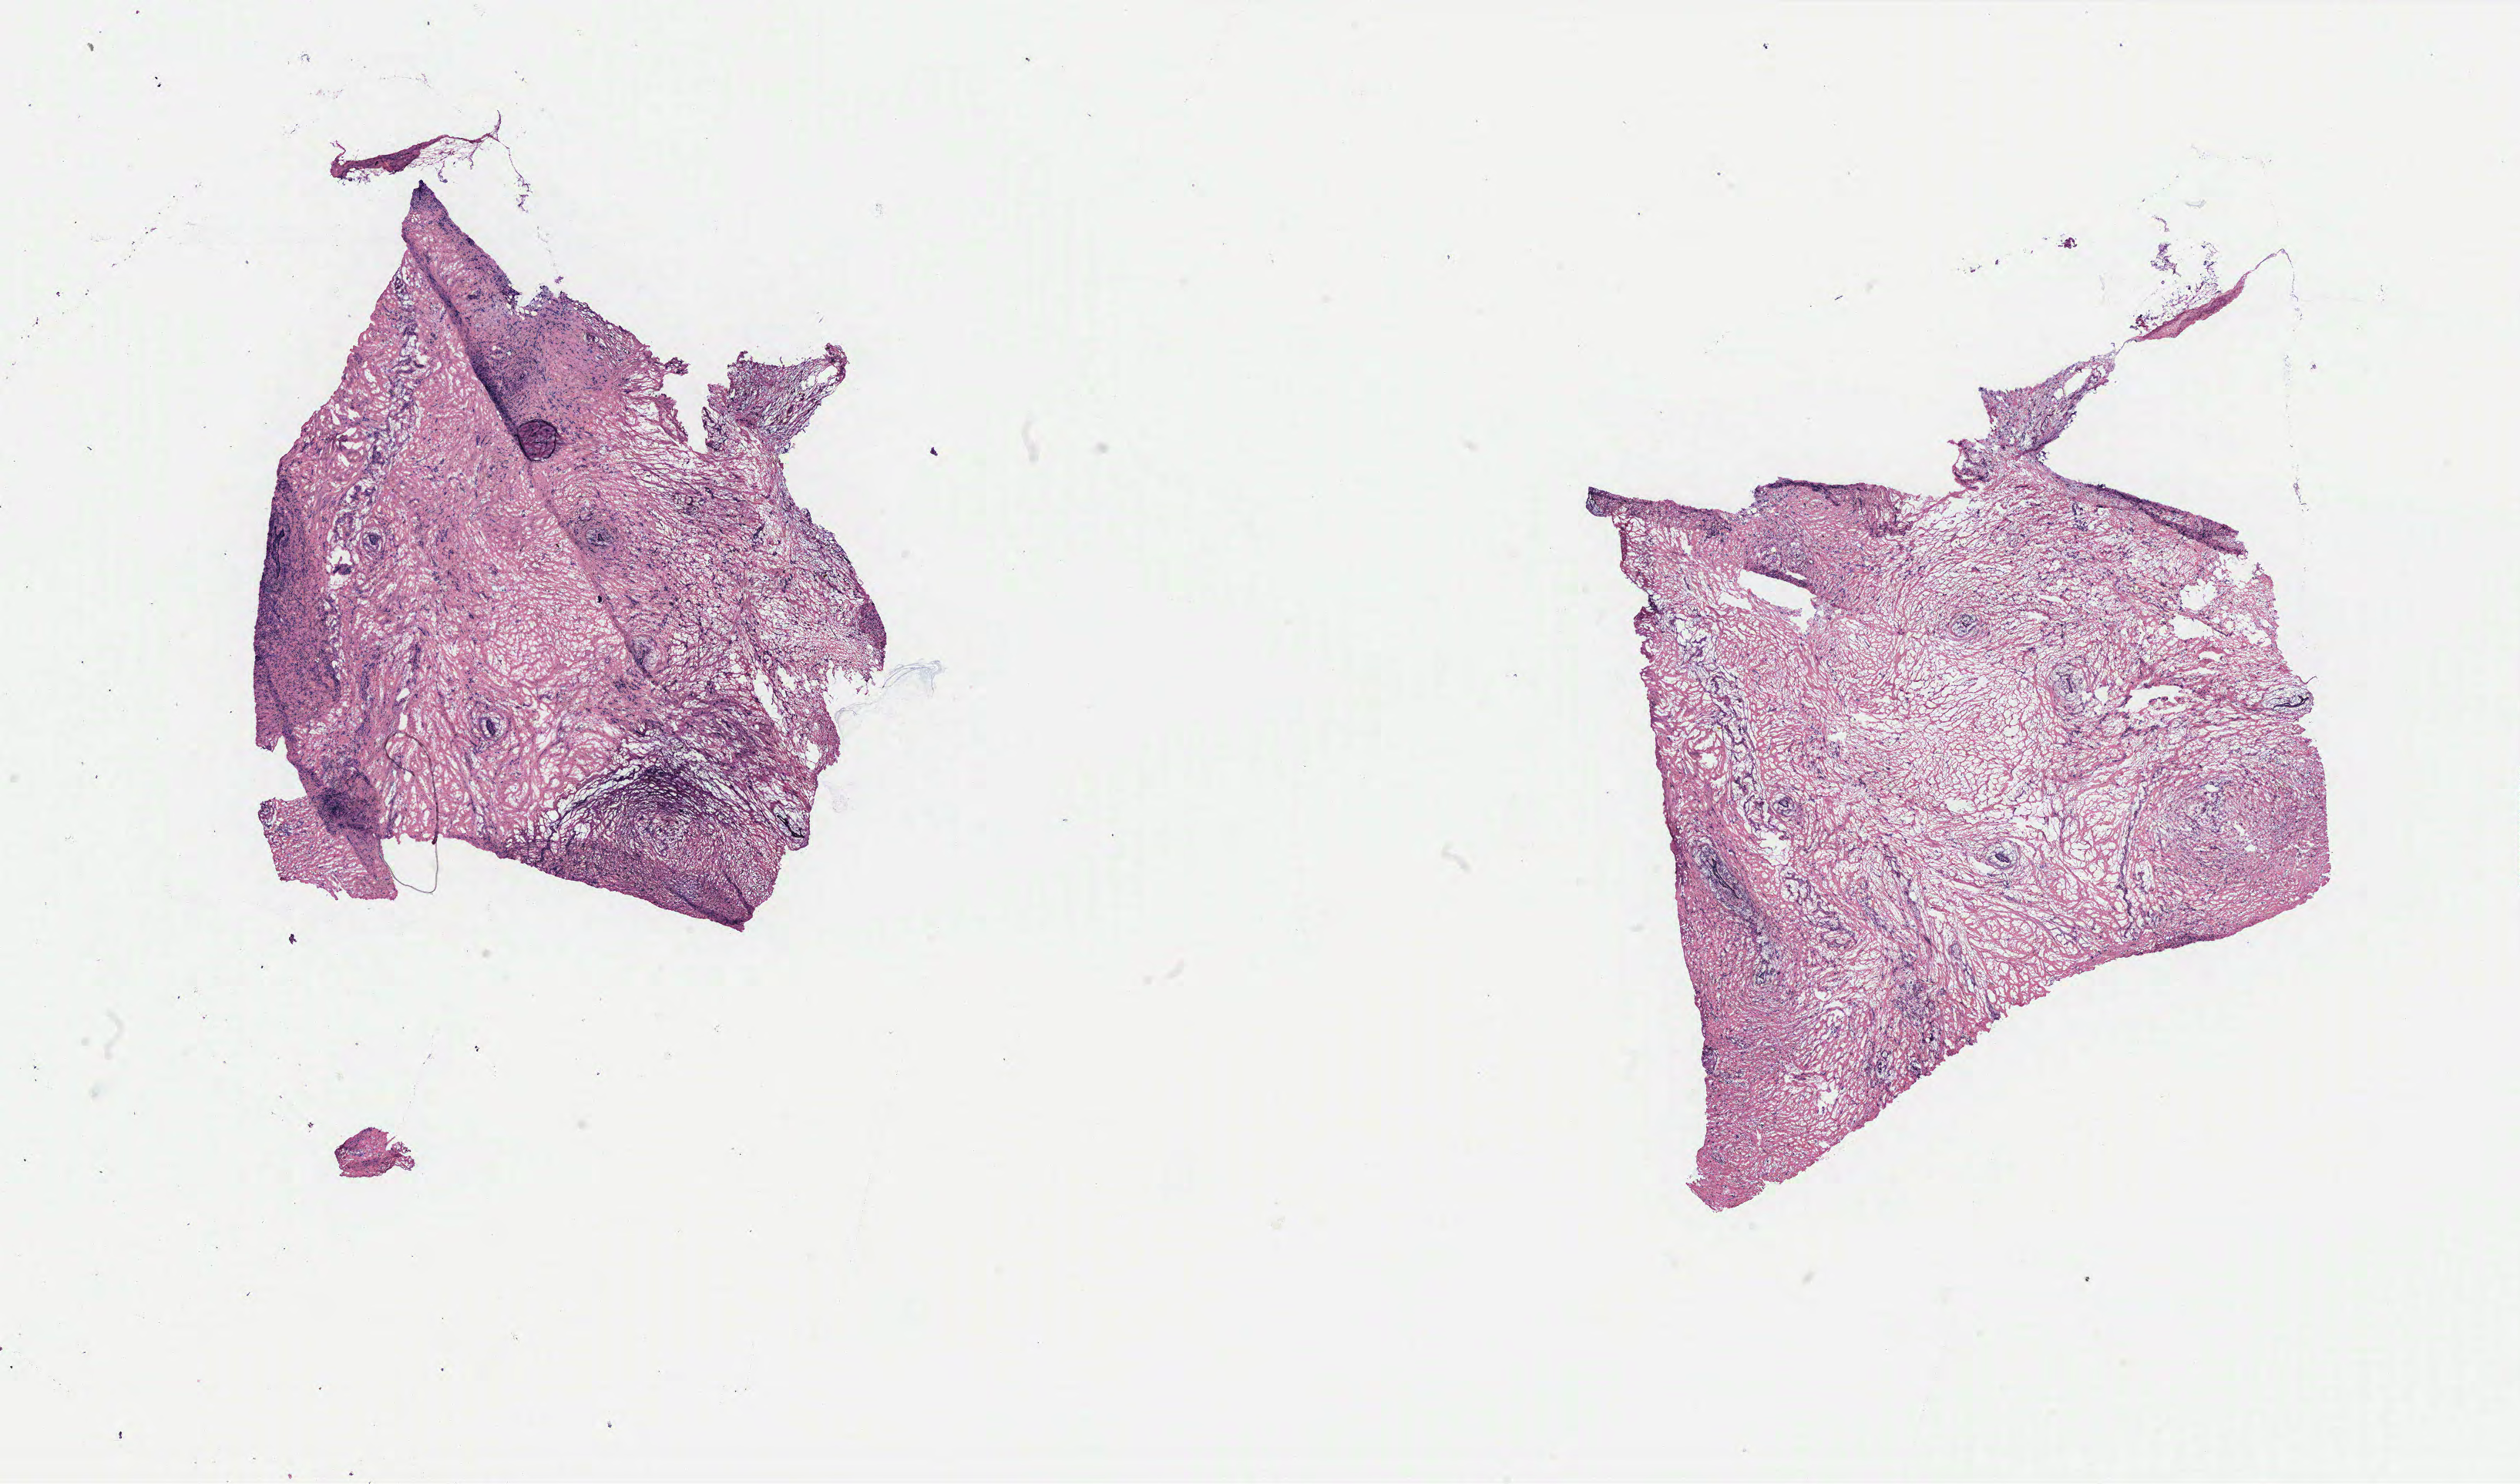
H&E whole-slide image, low-resolution overview of the scanned area, about 26.2 x 15.4 mm (acquisition: 40x scan), tumour tissue sample, breast. Female, 64 y/o.
* histologic diagnosis: Infiltrating lobular carcinoma, NOS
* AJCC pathologic stage: IIIC